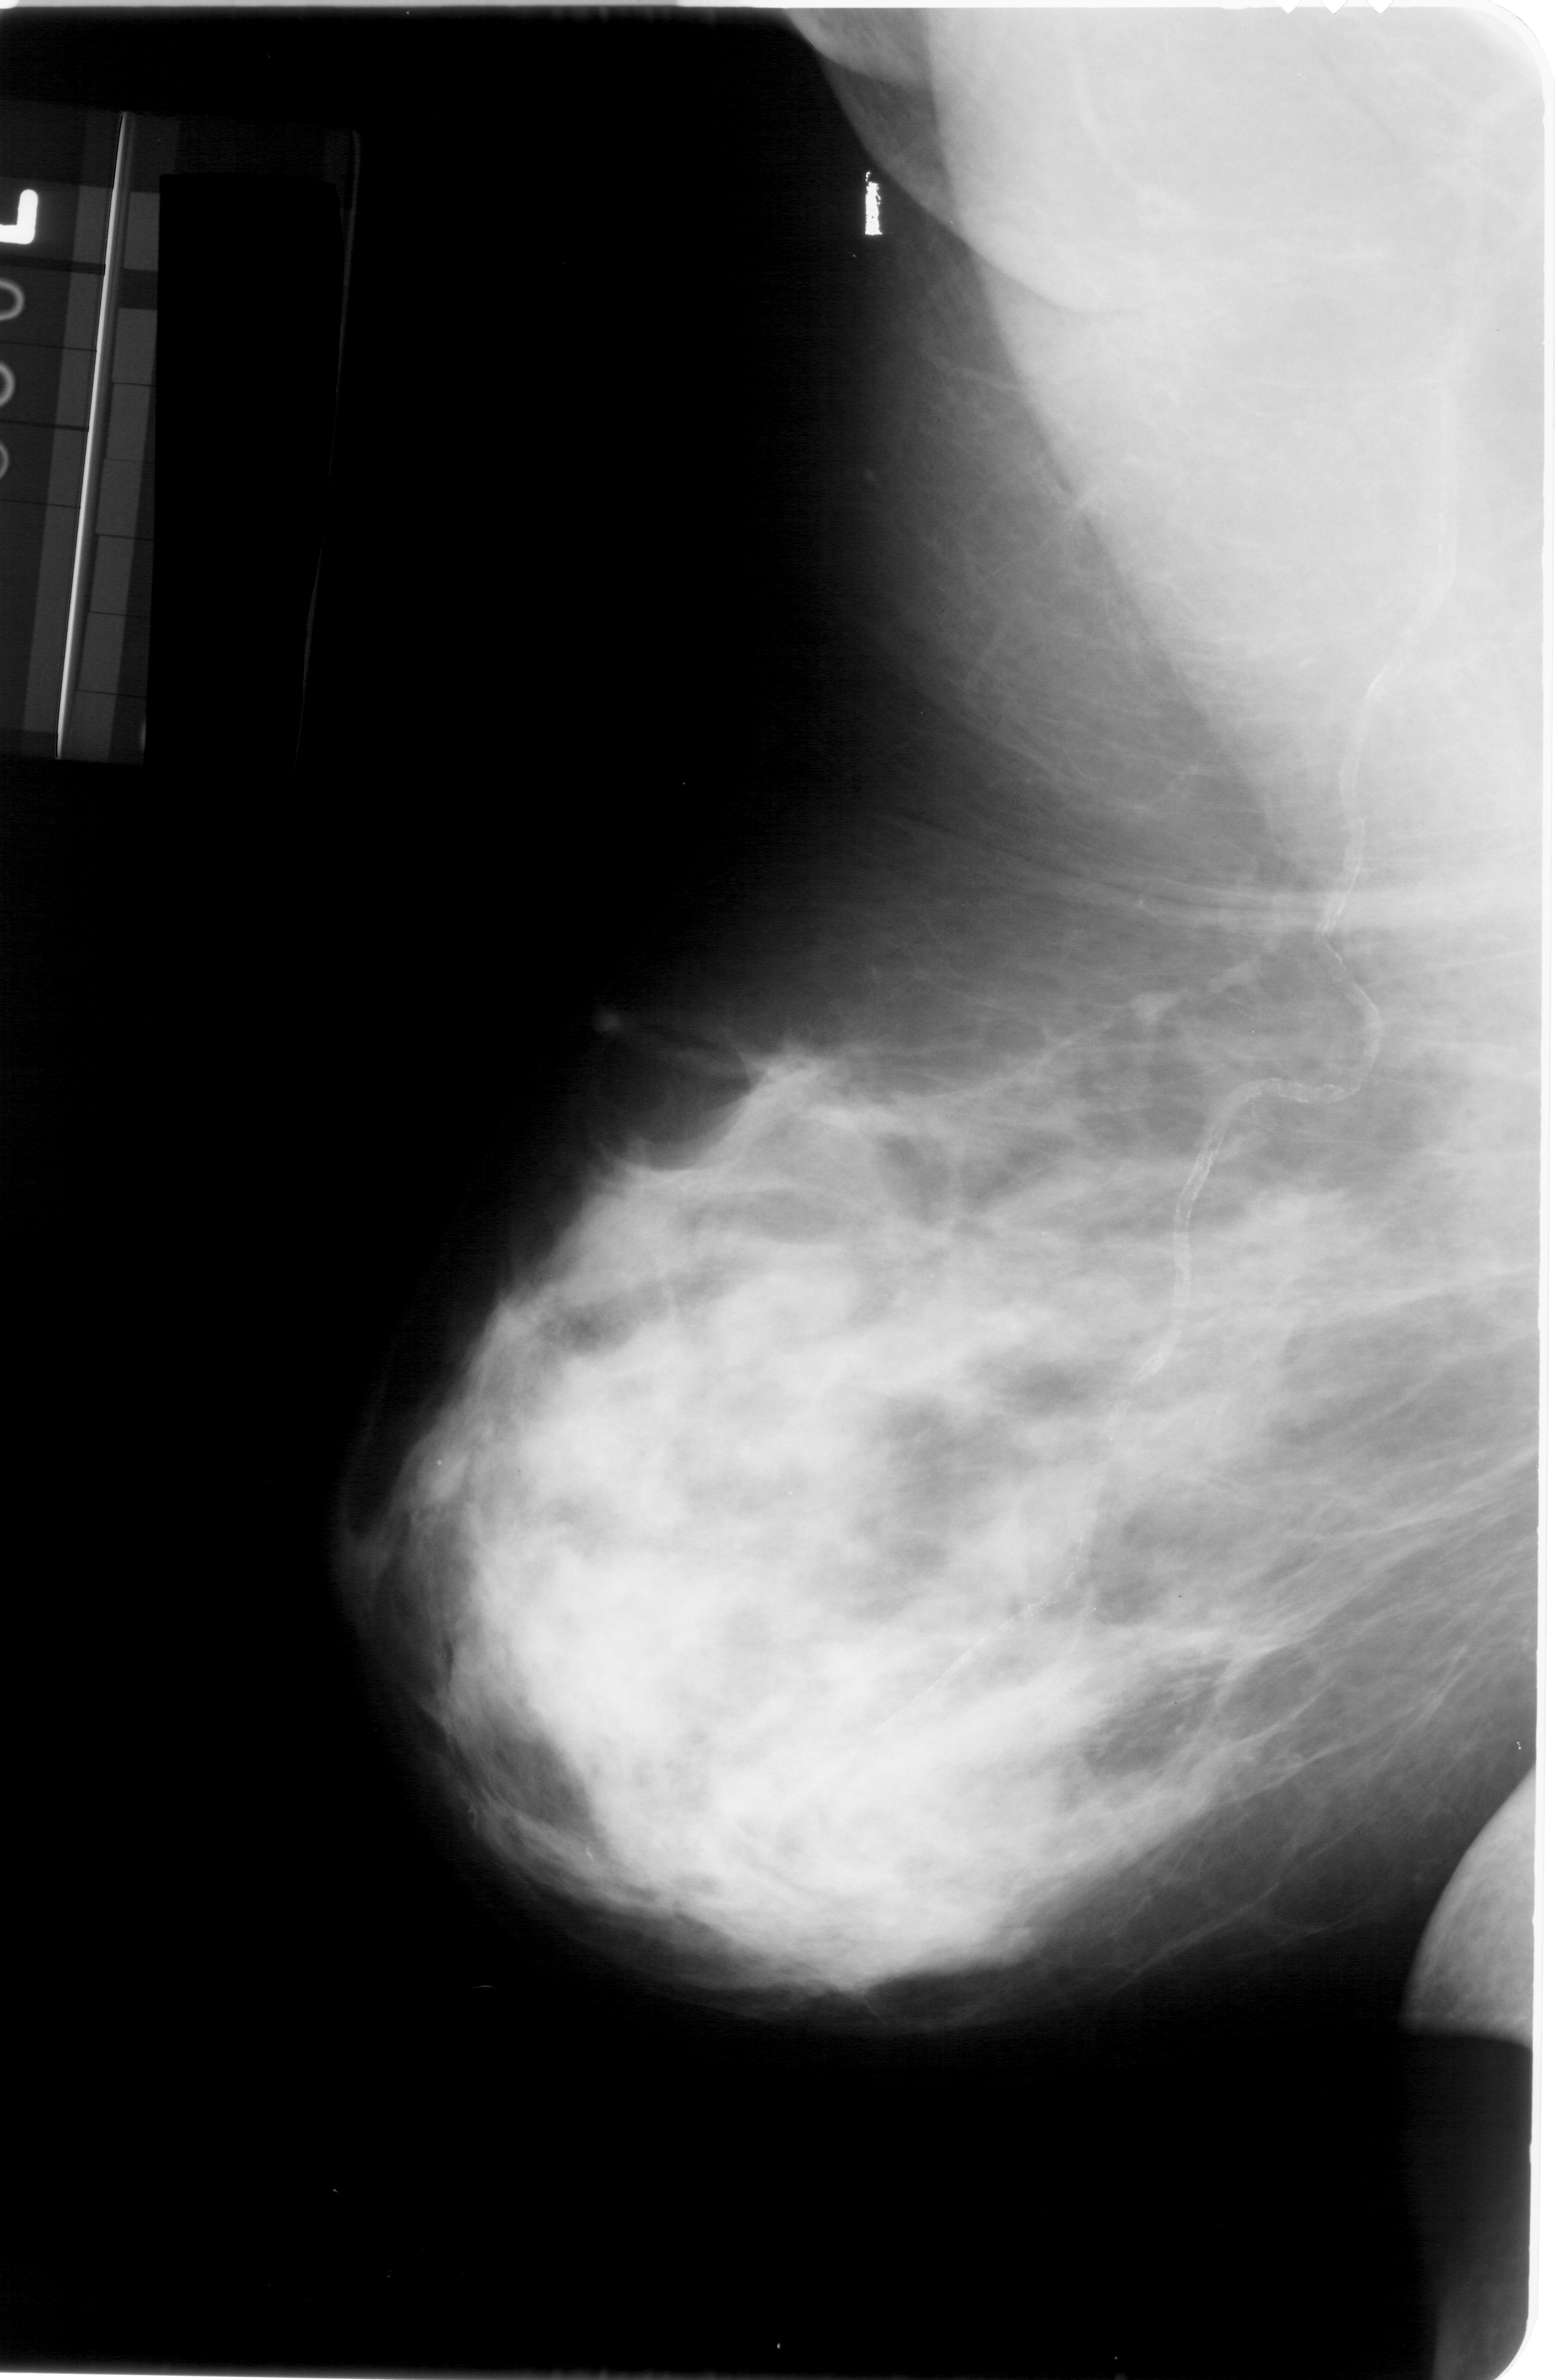
Scanned film-screen mammogram; left breast; MLO view.
Radiologist-marked abnormalities on this image: calcifications, morphology pleomorphic, distribution segmental; BI-RADS assessment category 4; subtlety rating 2 on a 1 (subtle) to 5 (obvious) scale; pathology result (as recorded, not read from the image): malignant.